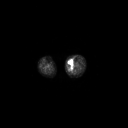
FDG PET of an extremity soft-tissue mass (from a PET/CT study), one axial slice; slice 130 of 223 in the series (ordered by position); 3.27 mm slice thickness; 128 × 128 image matrix. Patient: female, 70 years. From the clinical record (not read from this slice): histological type: extraskeletal high grade osteogenic sarcoma; grade: high; site of the primary tumour: left calf.
Structures marked on this image (expert contour drawn on MRI and transferred to this co-registered scan by the dataset authors):
- gross tumour volume (mass): bounding box [x1, y1, x2, y2] px = [68, 62, 73, 66]